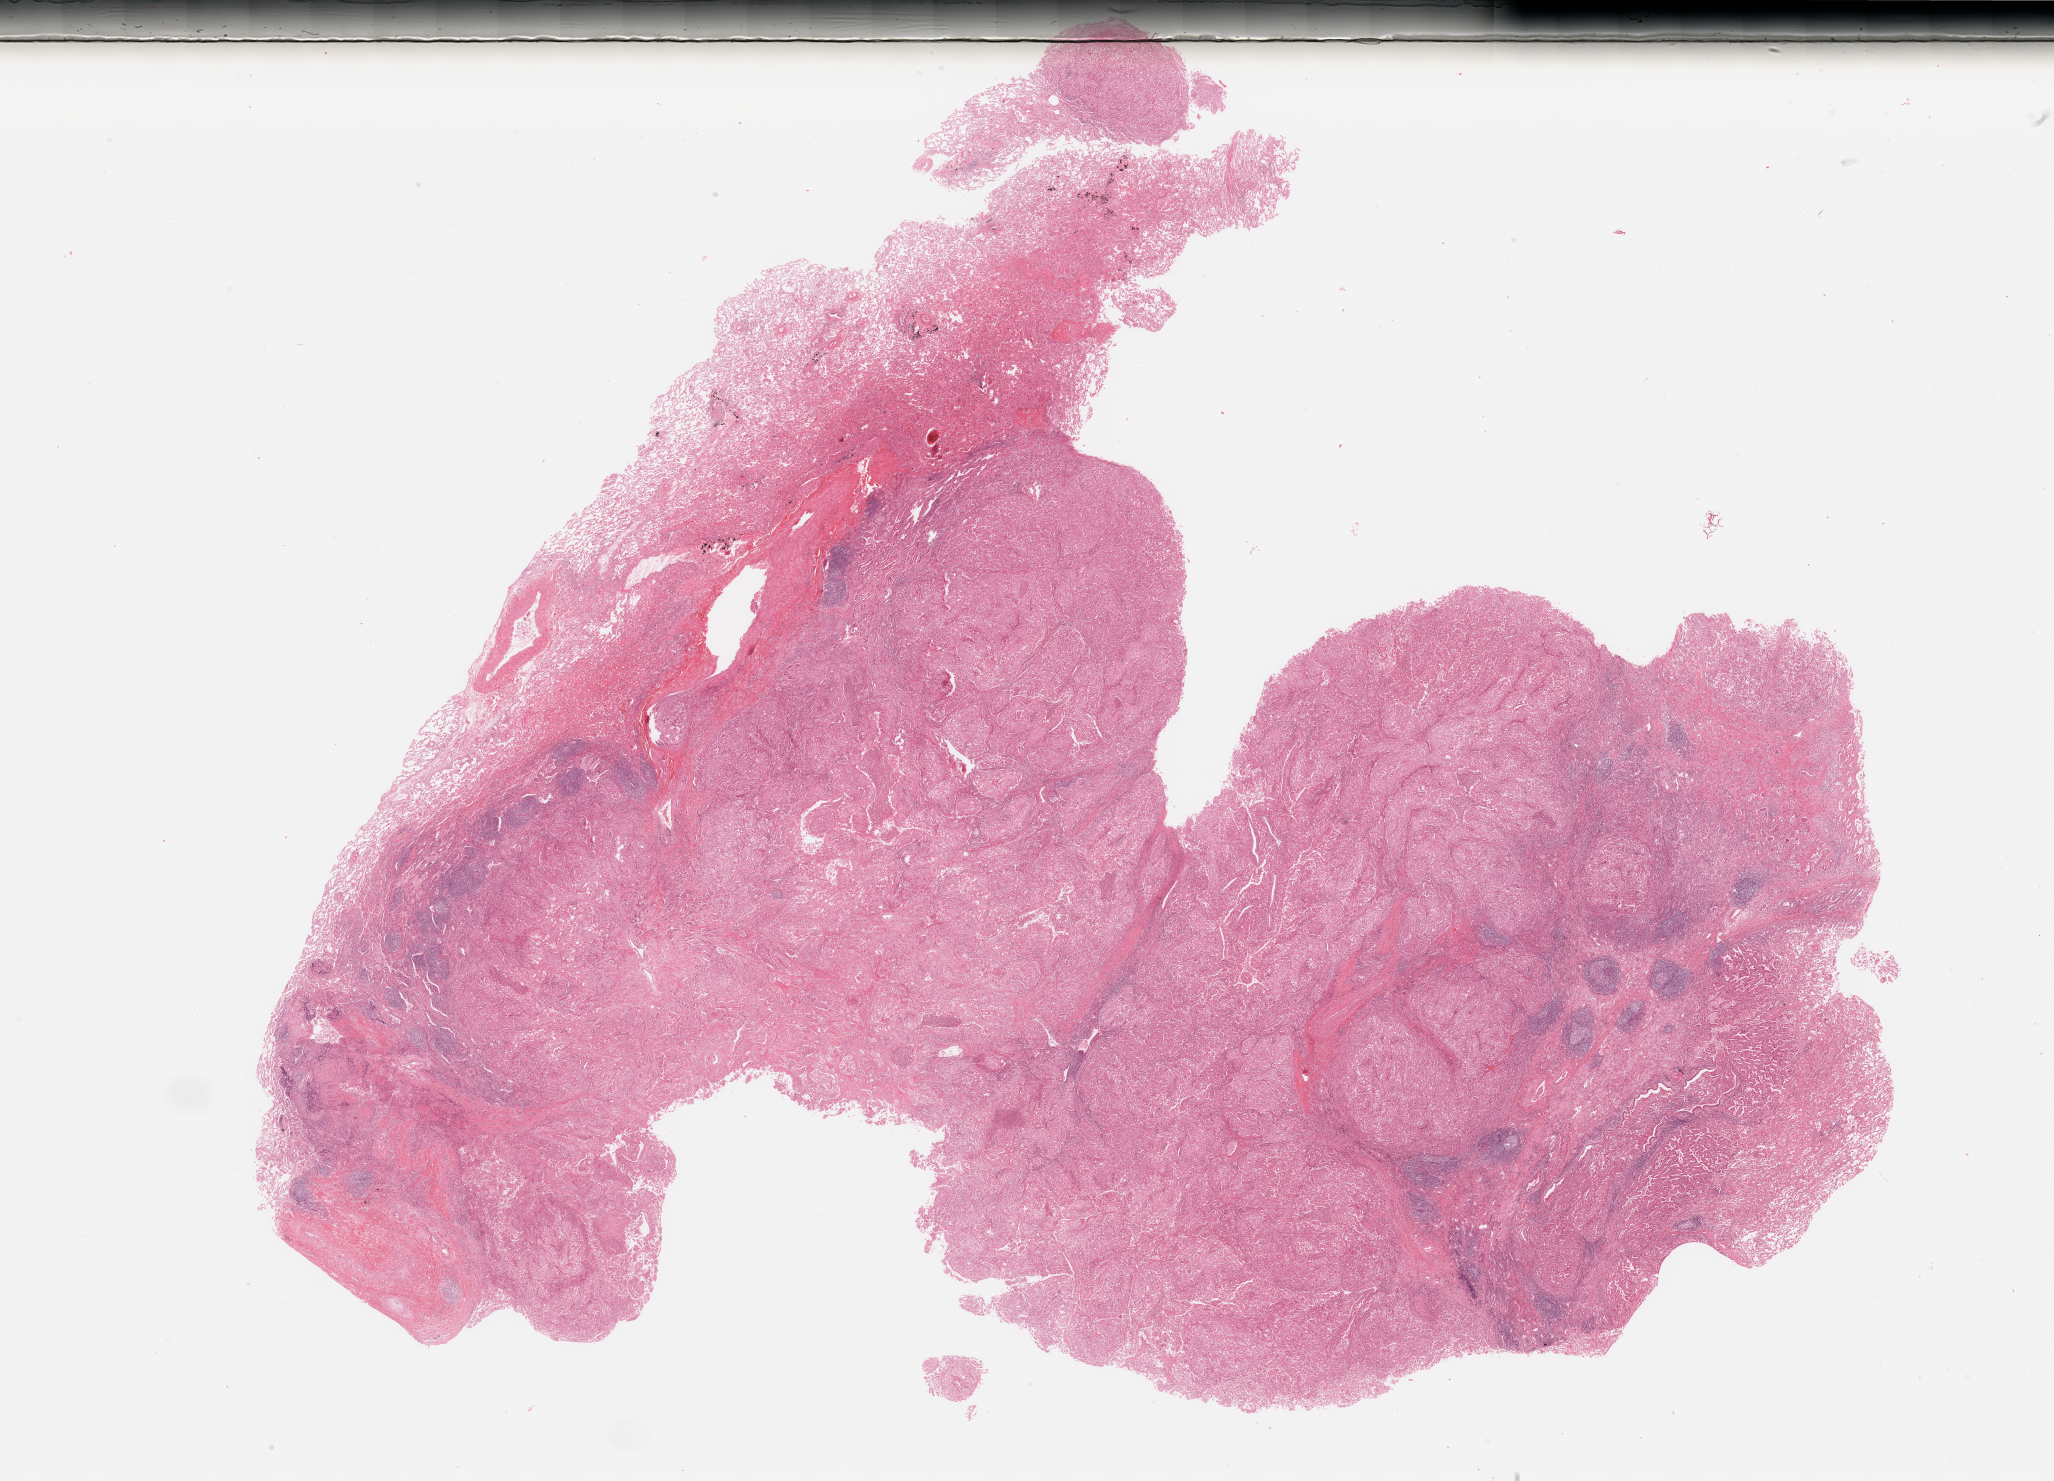
Whole-slide histology image, Hematoxylin and eosin (H&E) stained, shown as a low-resolution overview of the whole scanned area (about 32.5 x 23.4 mm, from a 20x scan); tumour tissue sample, lung. Female, 47 y/o. Histologic grade: G3 (poorly differentiated).
AJCC pathologic stage: IIIA. Histologic diagnosis: Adenocarcinoma, NOS.